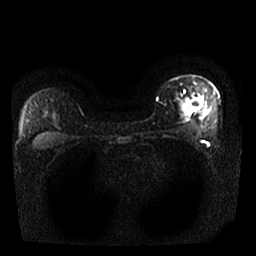
Breast MRI, one axial slice. Position 21 of 25 along the scan axis. Diffusion-weighted series; image 2 of 4 stored at this slice position (different b-values; order by instance number). 1.5 T. 4 mm slice thickness. 256 × 256 image matrix, field of view 320 × 320 mm. Female patient.
Structures marked on this image (manually delineated by an expert):
- tumour on diffusion-weighted imaging: box from (x=185, y=98) to (x=202, y=110) px